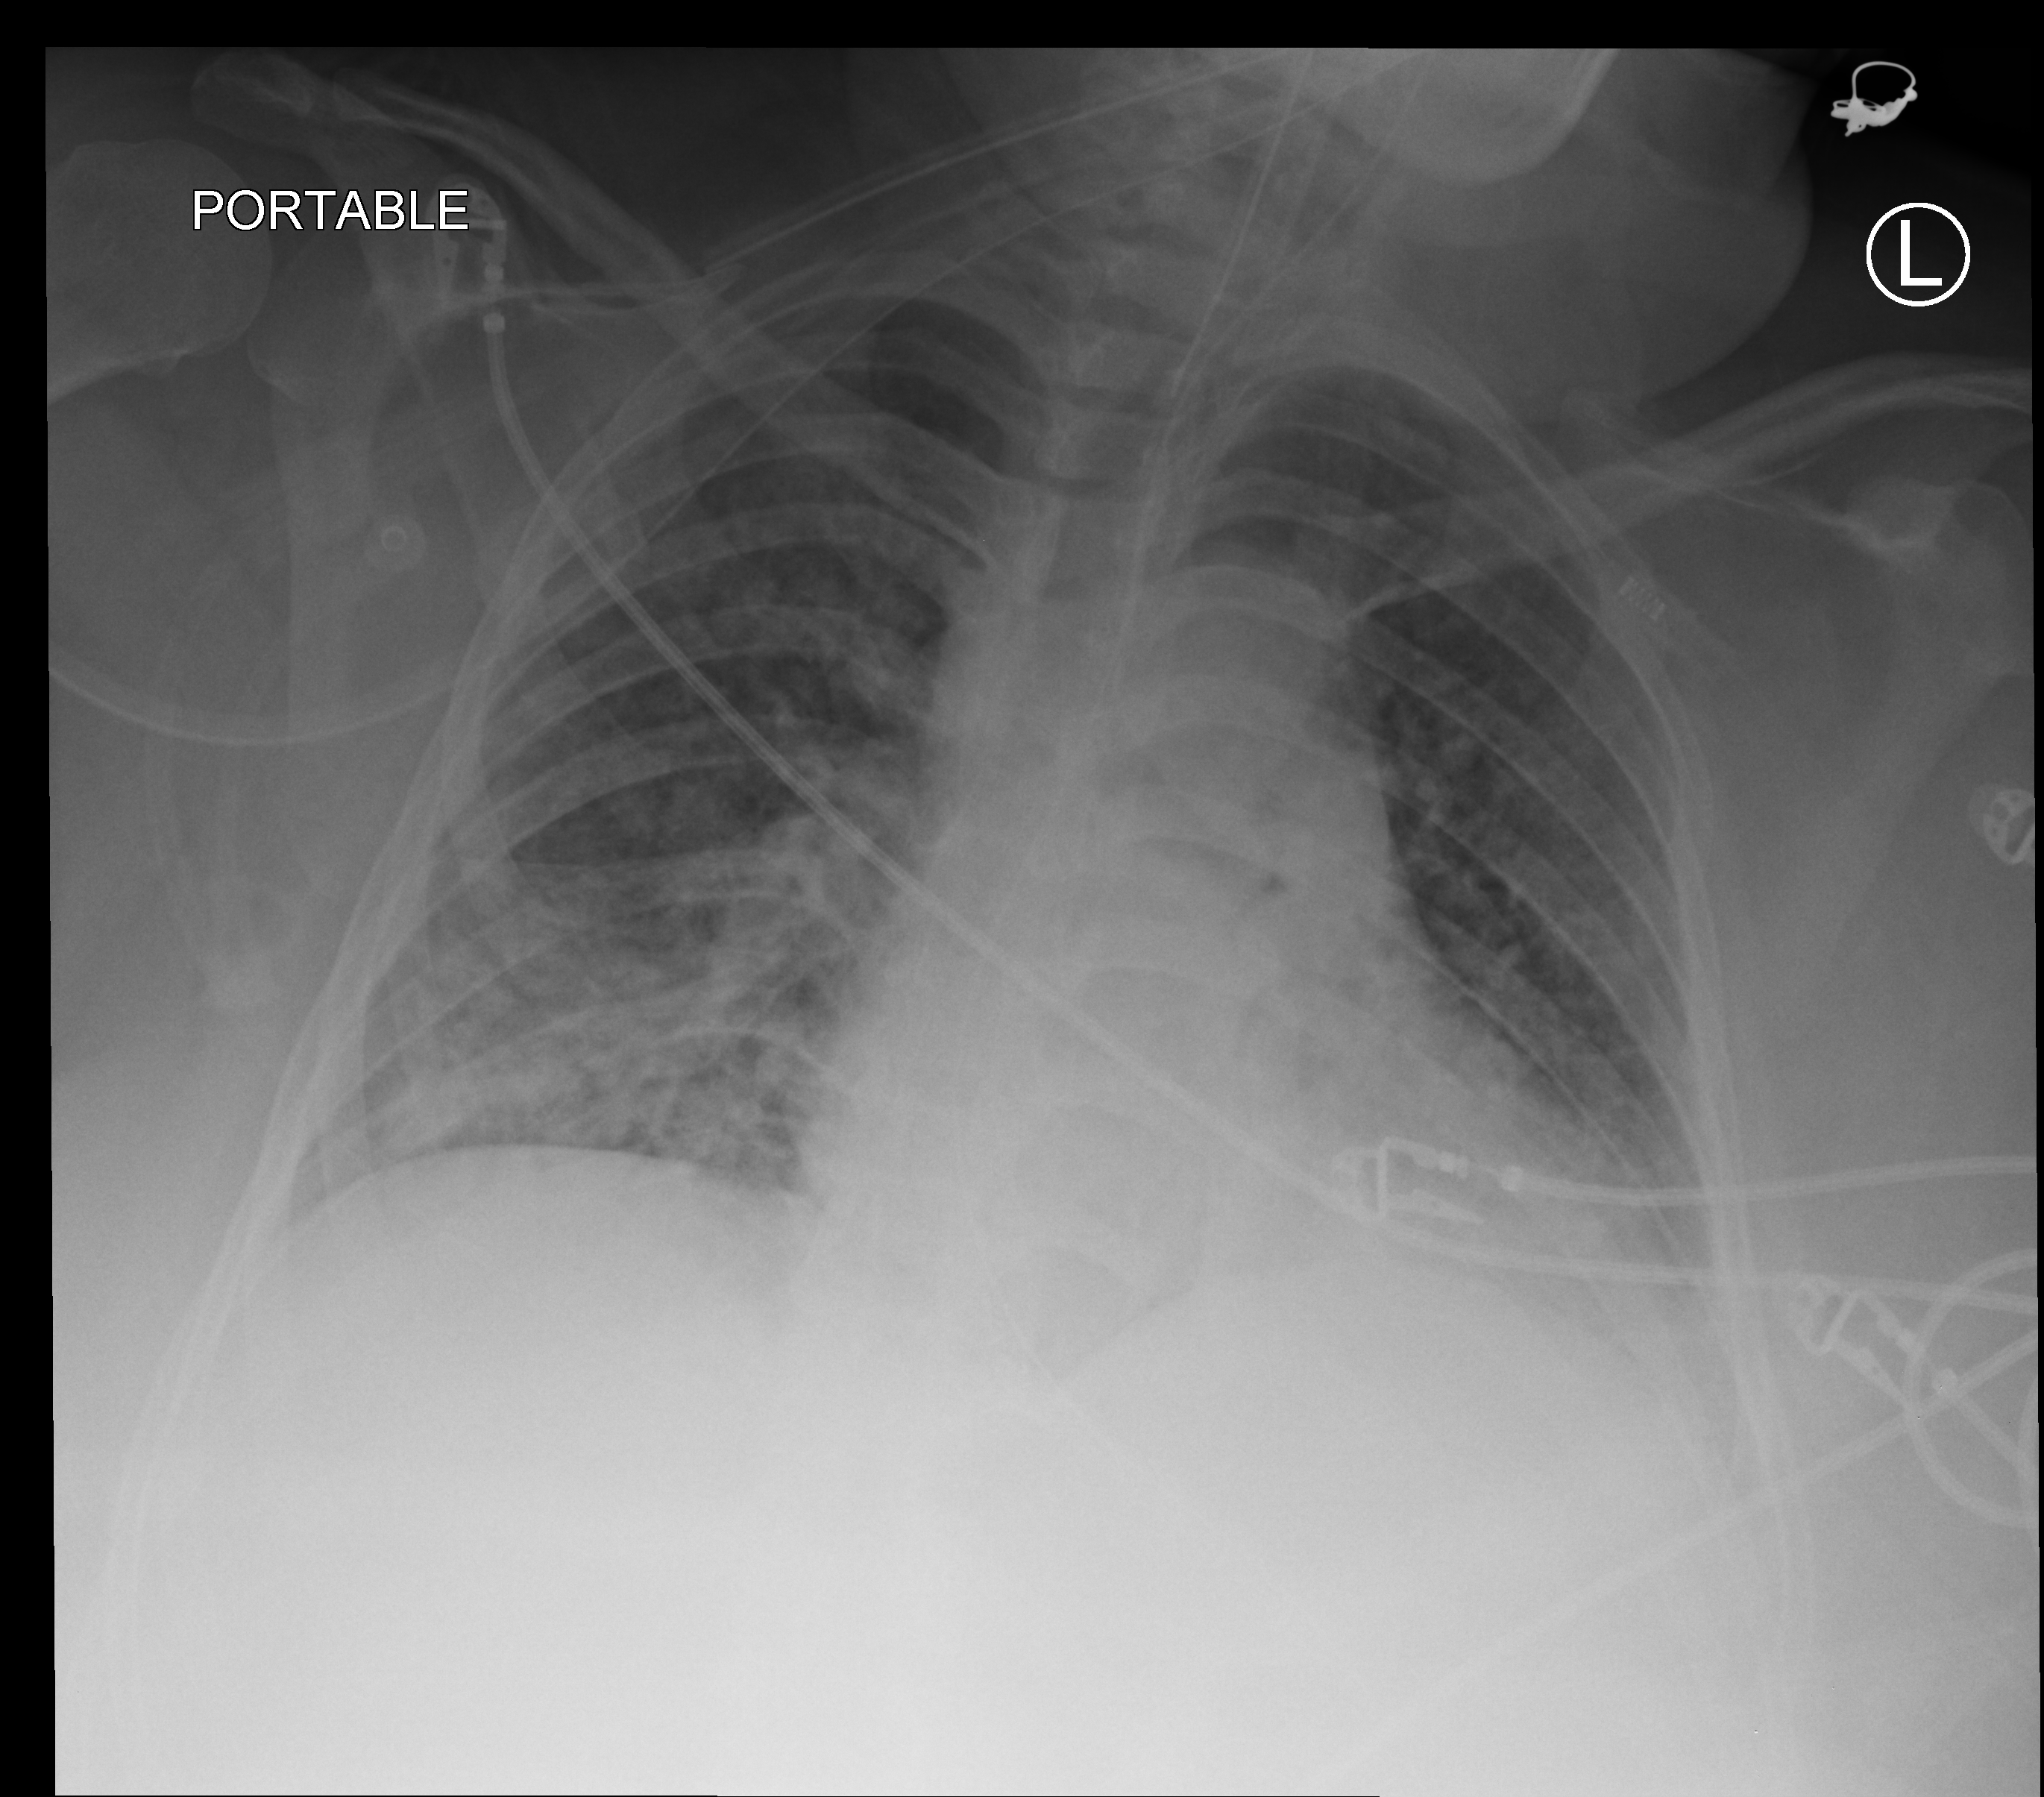
Bedside chest radiograph (computed radiography). Patient hospitalised with COVID-19; female, aged 18–59 years.
Hospital-stay facts (about this admission, not read from this image; timing relative to this image not recorded): hypertension (admission record): no; mechanically ventilated during this hospital stay: yes; other chronic lung disease (admission record): no.